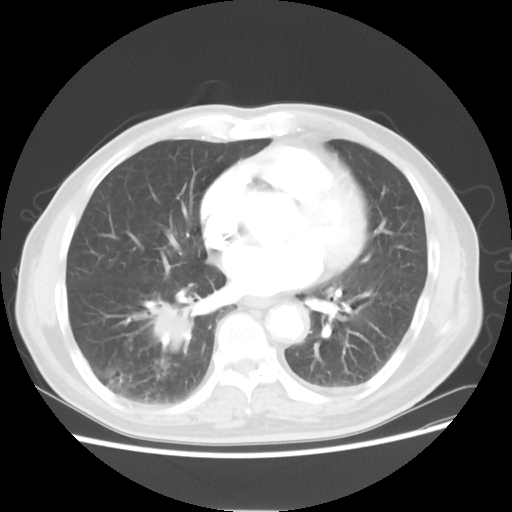
Chest CT, one axial slice; position 26 of 58 along the scan axis; 120 kVp; lung window (W 1500 / L -600 HU); 5 mm slice thickness; 512 × 512 image matrix, field of view 360 × 360 mm. Patient: male, 74 years. Case-level facts recorded for this patient, not image findings: clinical TNM (as recorded): T1c N1 M1.
Outlined on this slice (rectangle marked by the reading radiologist):
- lung tumour (recorded histology: adenocarcinoma): bounding box [x1, y1, x2, y2] px = [135, 292, 198, 361]